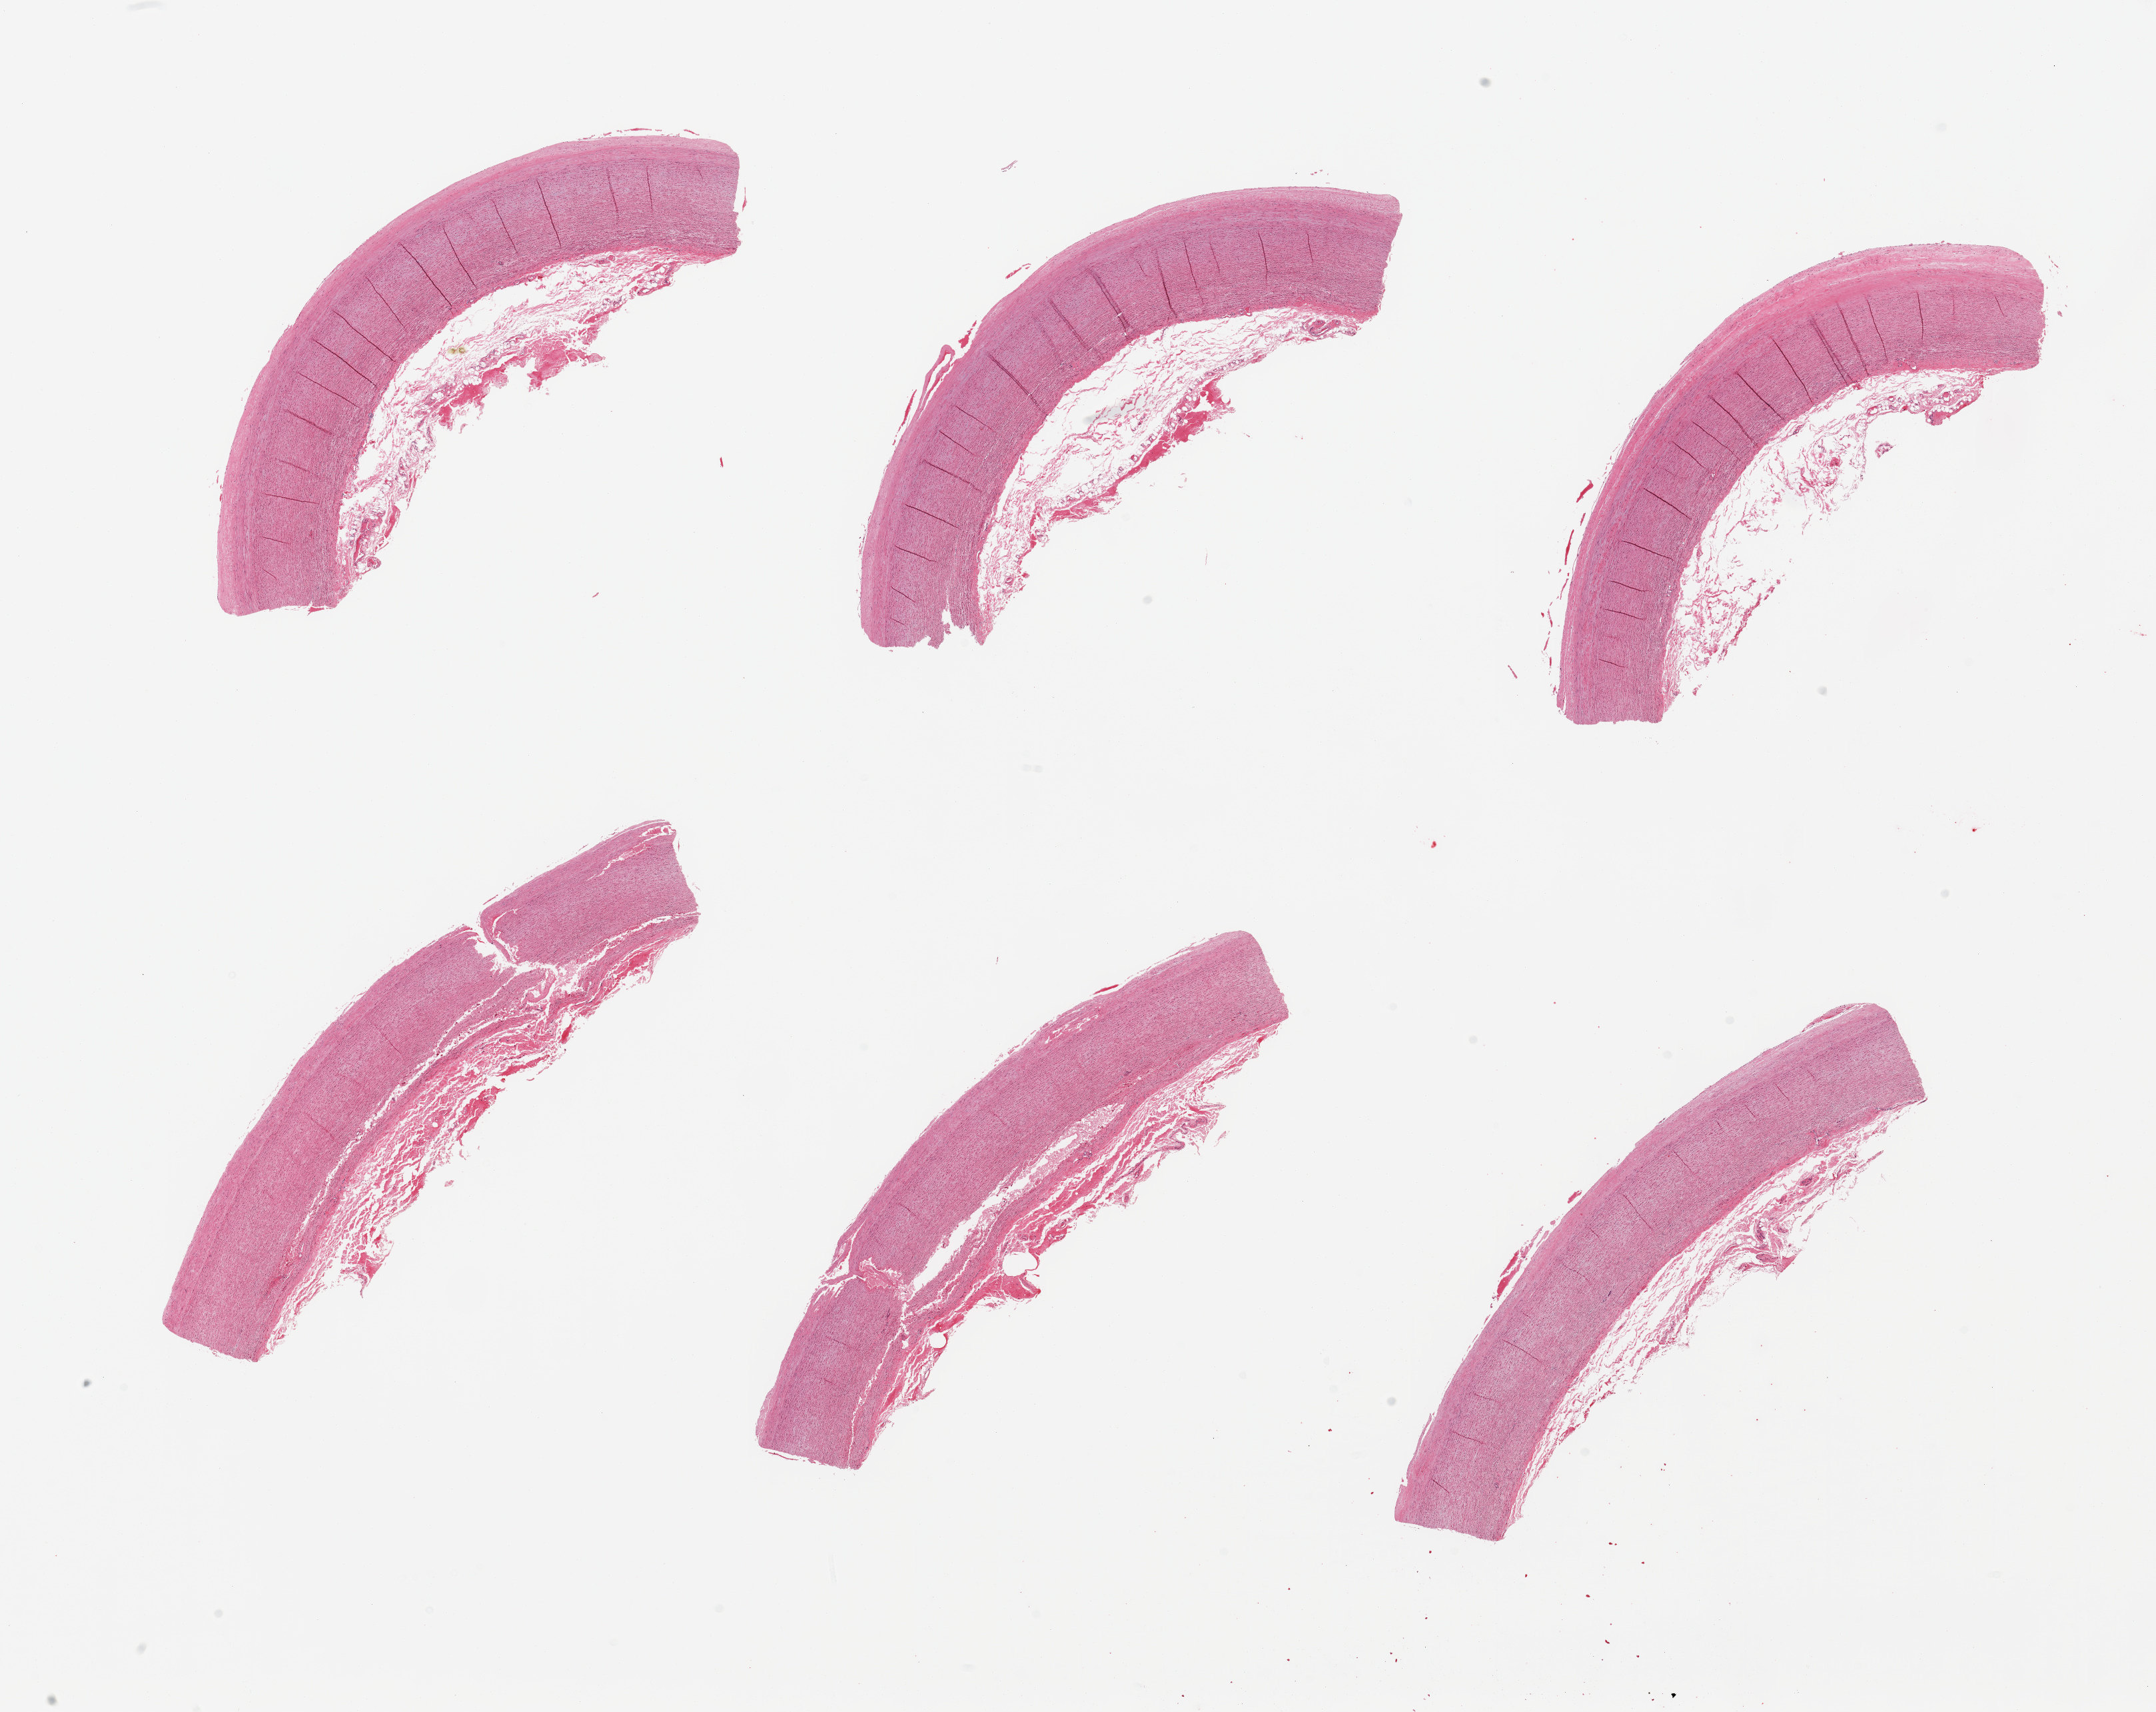
Digitized haematoxylin and eosin-stained section — low-resolution overview of the scanned area, about 25.6 x 20.3 mm. PAXgene-fixed, paraffin-embedded tissue. Section of aorta (target tissue). Tissue donor sample. Donor sex: male.
Reviewer comment on this tissue sample: 6 pieces, atherosis up to ~0.15mm.